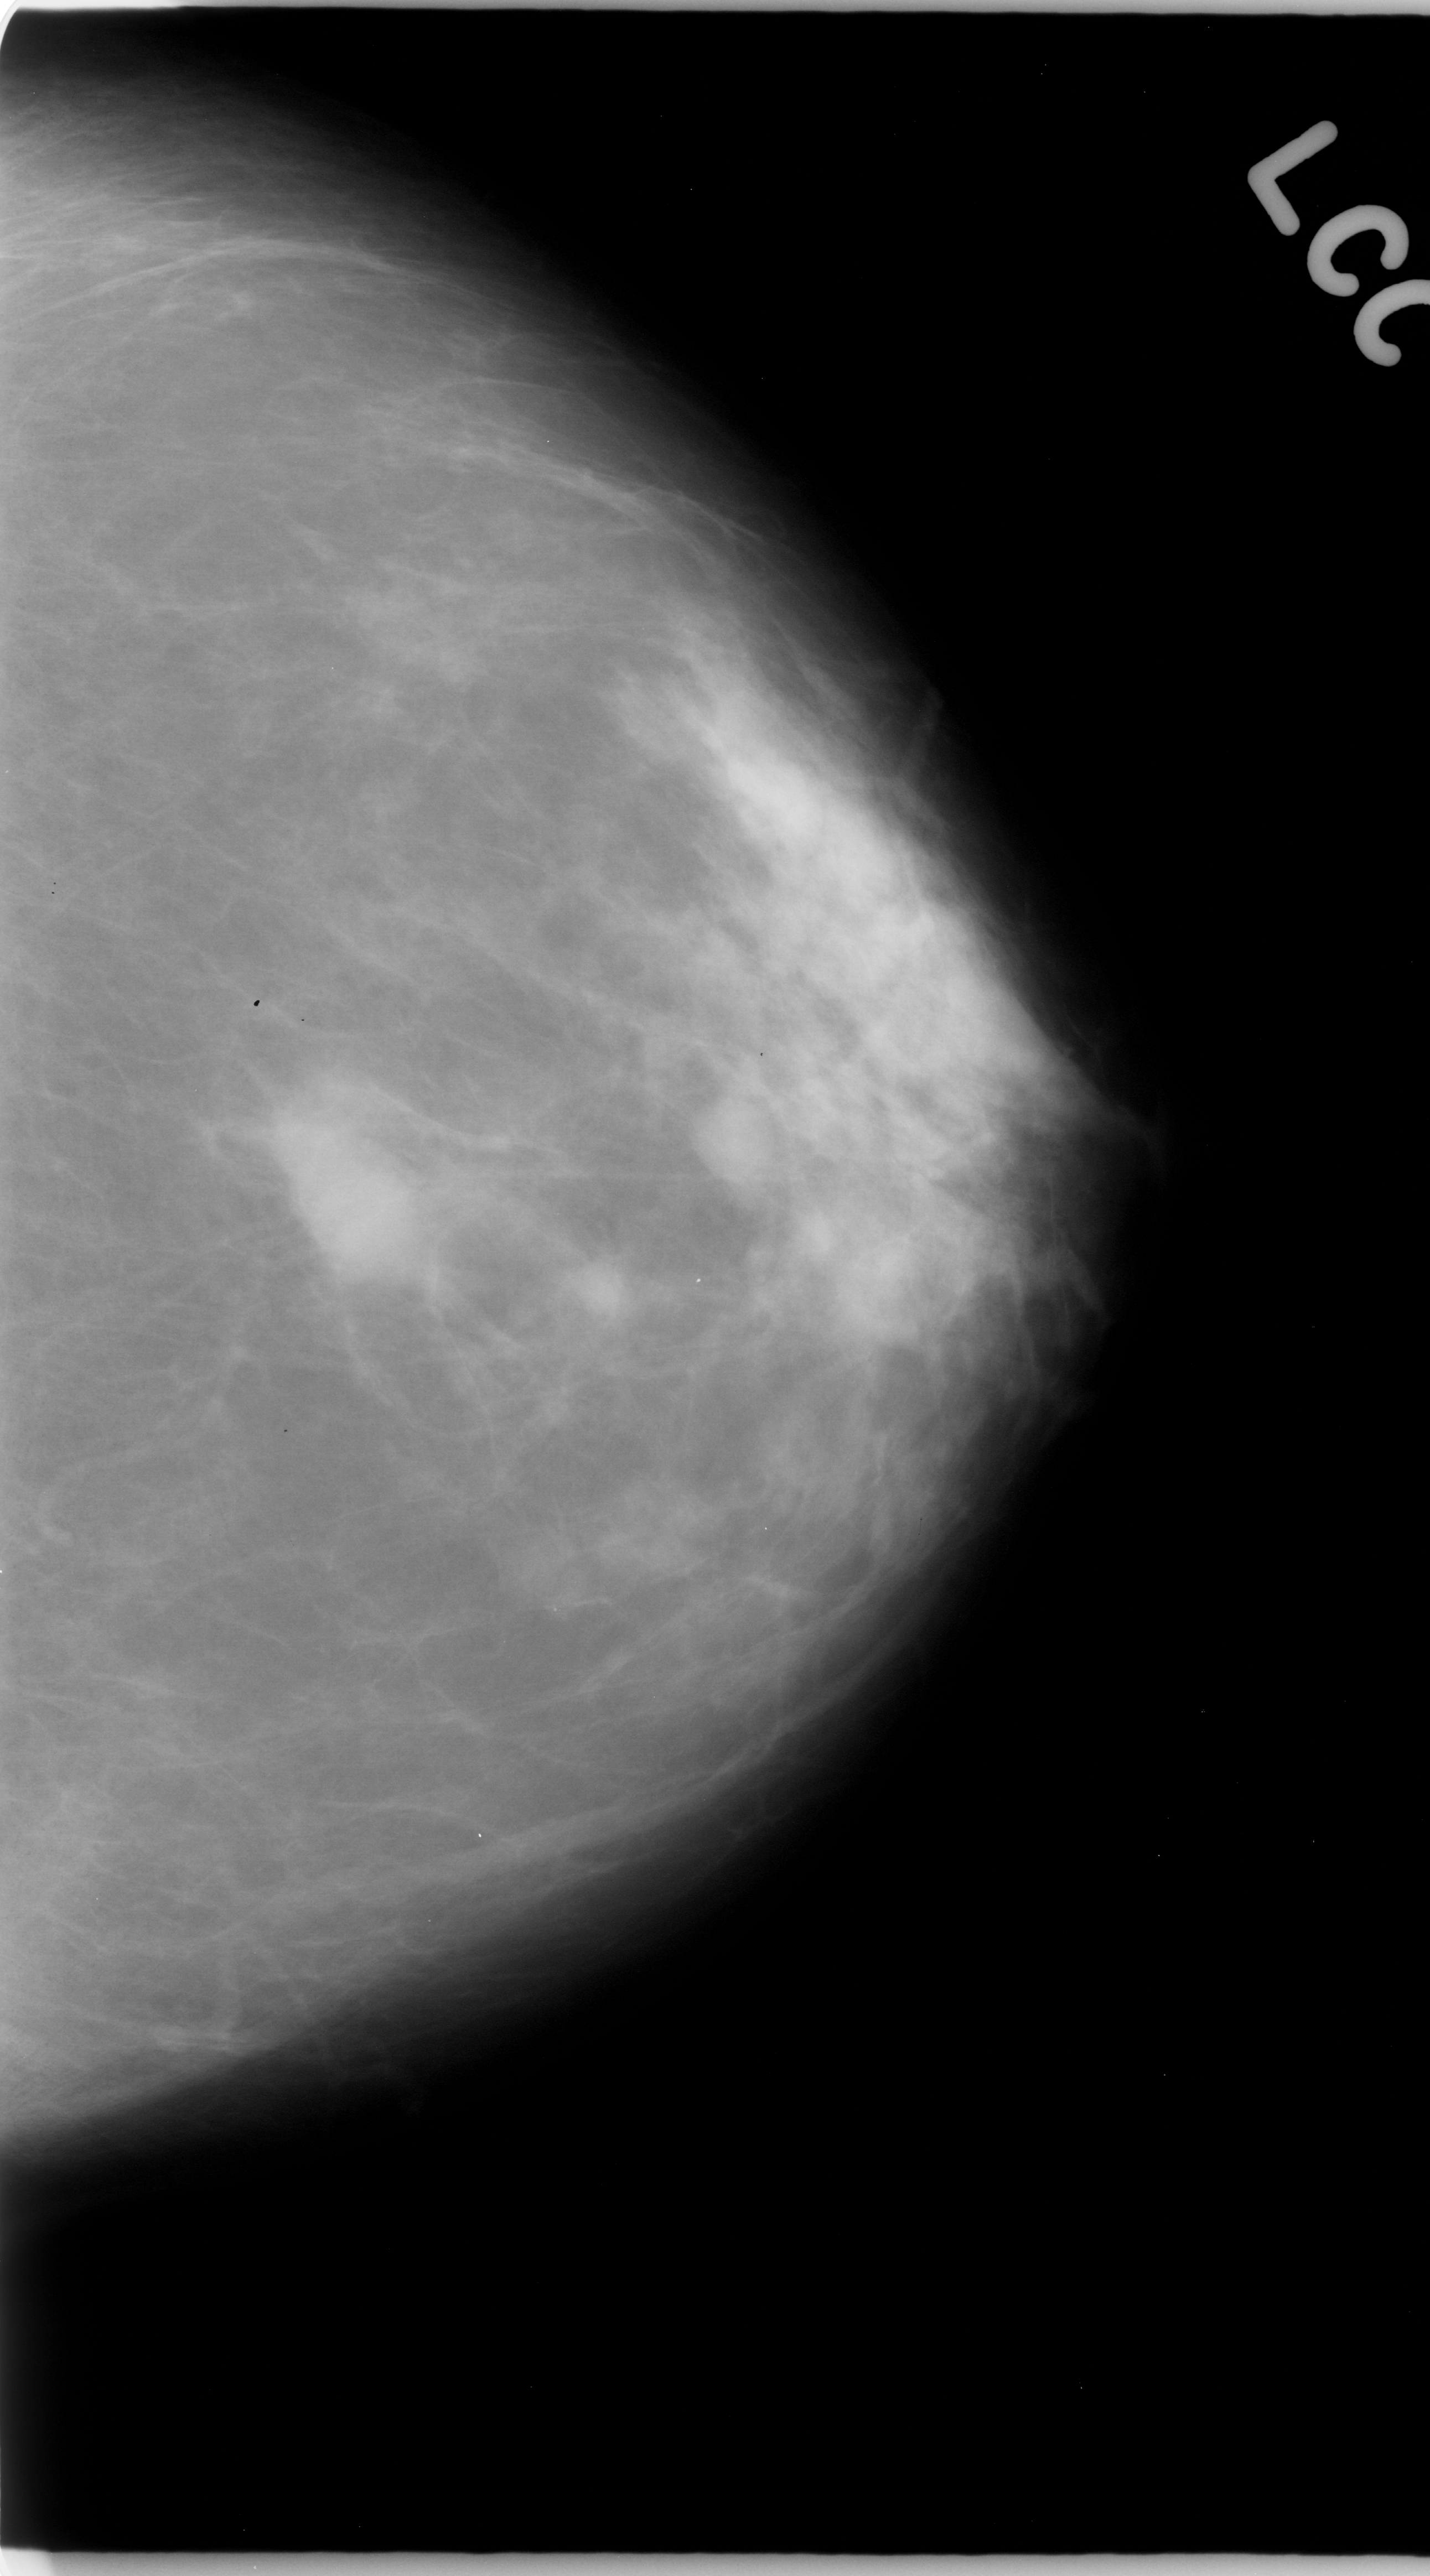
Scanned film-screen mammogram; left breast; craniocaudal (CC) view; breast composition: scattered fibroglandular densities (BI-RADS density category 2 of 4).
- Marked findings (only marked abnormalities are described; nothing is implied about the rest of the image): Finding 1 of 2: mass, shape oval, margins circumscribed; BI-RADS assessment category 3; pathology result (as recorded, not read from the image): benign.
- Finding 2 of 2: mass, margins ill defined; BI-RADS assessment category 5; subtlety rating 5 on a 1 (subtle) to 5 (obvious) scale; pathology result (as recorded, not read from the image): malignant.